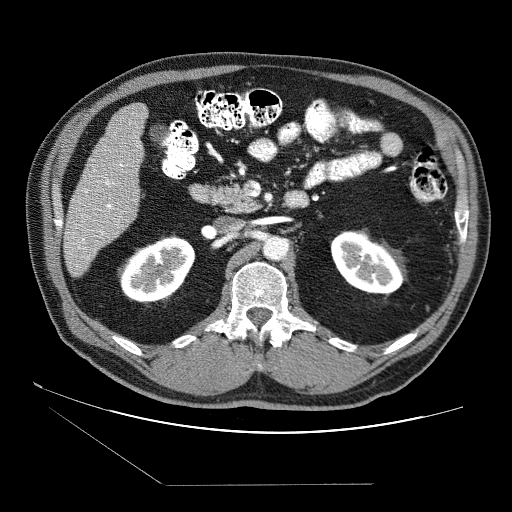
Contrast-enhanced abdominal CT (liver protocol), one axial slice; position 23 of 87 along the scan axis; reconstruction kernel STANDARD; 120 kVp; soft-tissue window (W 400 / L 40 HU); 2.5 mm slice thickness; 512 × 512 image matrix, field of view 400 × 400 mm. From the clinical record (not read from this slice): diagnosis: hepatocellular carcinoma (patient treated with transarterial chemoembolisation; whether this scan precedes or follows treatment is not stated here); TNM stage (as recorded): Stage-II; Child-Pugh class: B; tumour differentiation: no biopsy; tumour size: 2.6 cm.
Structures marked on this image (semi-automatically segmented with operator editing):
- liver parenchyma outside the tumour (the mass and vessels are separate outlines, so this box may not span the whole liver): bounding box <64,104,148,276> (left, top, right, bottom; pixels)
- liver vessels: <78,122,140,251>